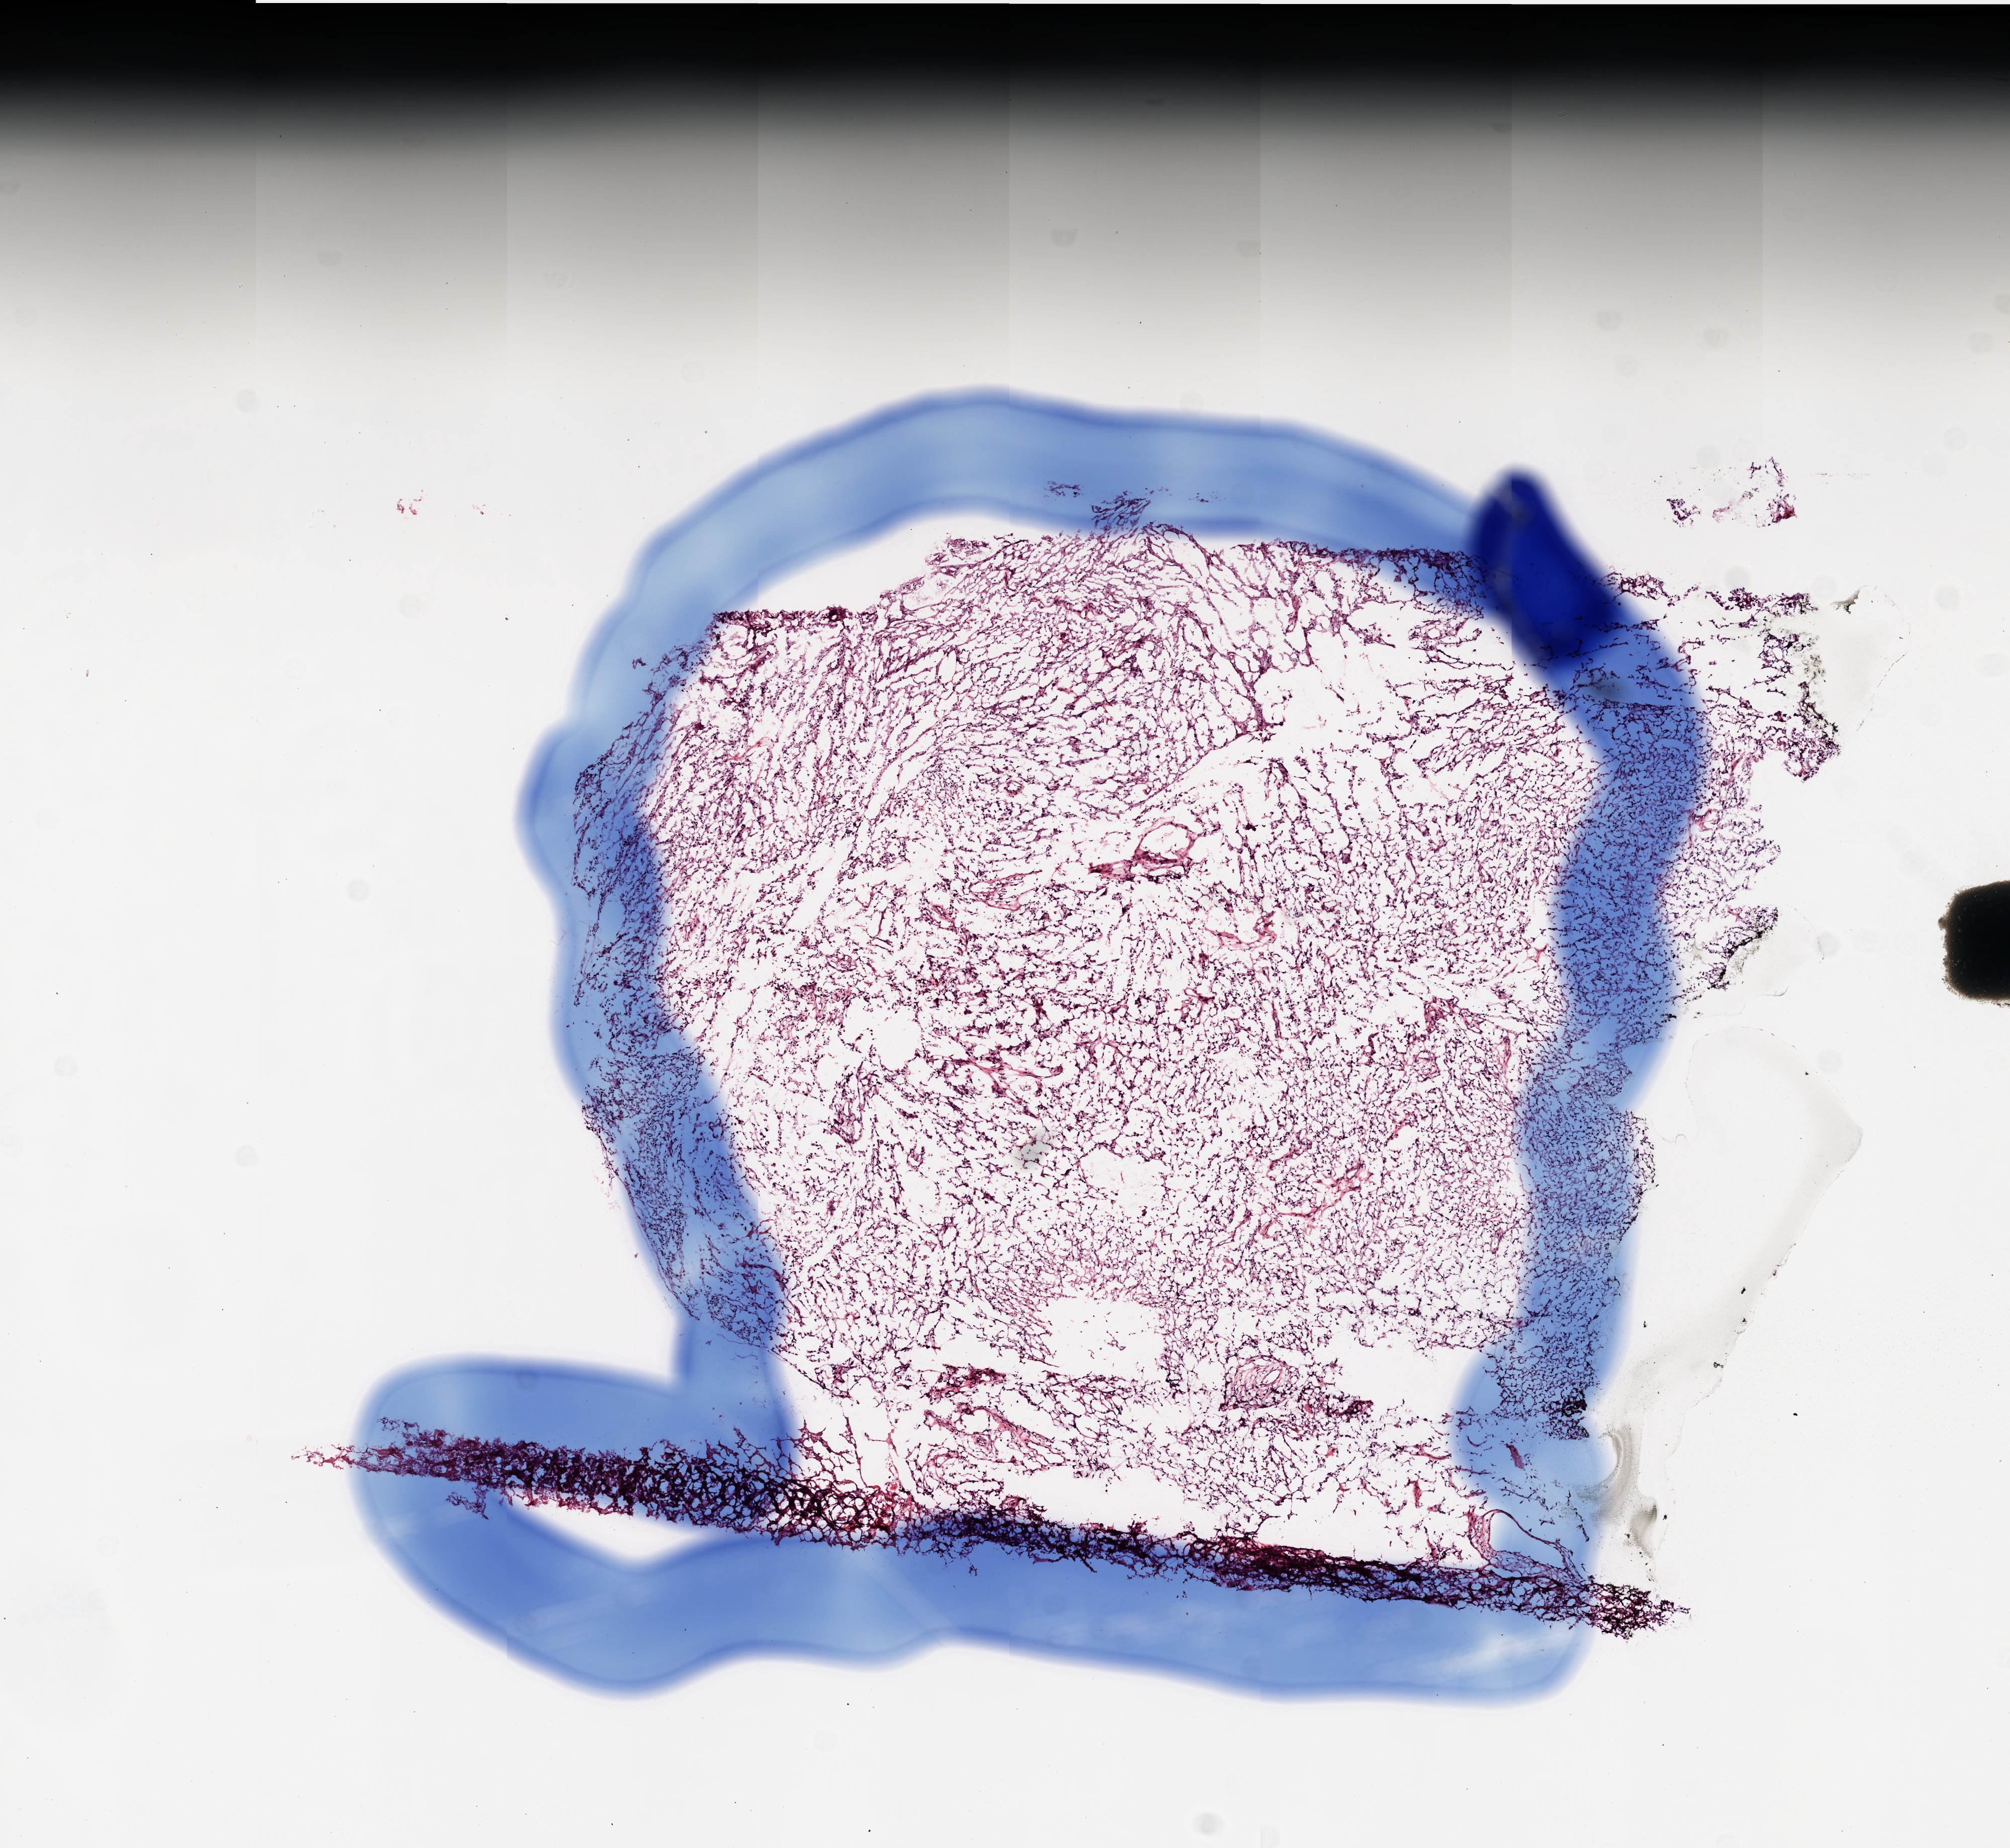
Digitized H&E-stained tissue section (whole slide) — a low-resolution overview of the entire scanned area, about 8.0 x 7.3 mm (from a 20x scan). Frozen section from the top of the tissue portion. Sample: primary tumour, brain. Male patient; age at initial diagnosis 67 years. Slide review estimates, as recorded: tumour cells 100%, tumour nuclei 100%, normal cells 0%, stromal cells 0%, necrosis 0%.
• histologic diagnosis: Glioblastoma